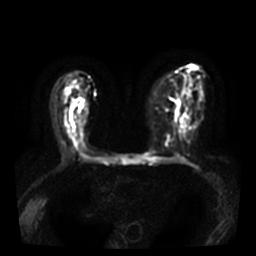
Breast MRI, one axial slice. Position 16 of 36 along the scan axis. Diffusion-weighted series; image 2 of 4 stored at this slice position (different b-values; order by instance number). 3 T. 5 mm slice thickness. 256 × 256 image matrix, field of view 320 × 320 mm. Female patient.
Annotated regions visible in this slice (outlined manually by an expert reader):
- tumour on diffusion-weighted imaging: bounding box [x1, y1, x2, y2] px = [73, 103, 76, 106]